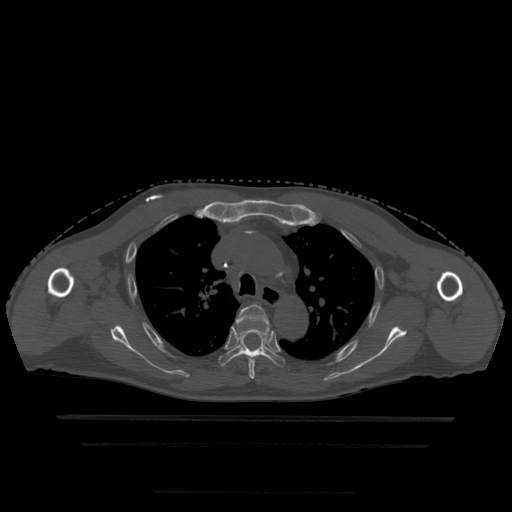
CT including the spine, one axial slice; position 344 of 522 along the scan axis; bone window (W 1800 / L 400 HU); 1.25 mm slice thickness; 512 × 512 image matrix, field of view 436 × 436 mm. Patient age 68 years. Case-level facts recorded for this patient, not image findings: primary cancer: urothelial.
Structures marked on this image (semi-automatically segmented with operator editing):
- T4 vertebra: bounding box [x1, y1, x2, y2] px = [236, 305, 270, 379]
- T5 vertebra: [219, 321, 285, 367]